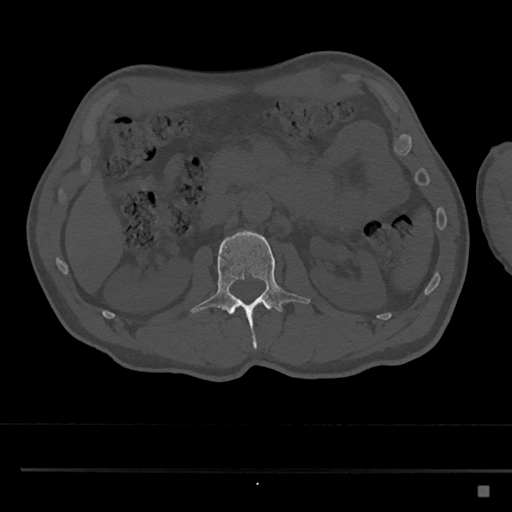
CT including the spine, one axial slice; slice 766 of 797 in the series (ordered by position); 120 kVp; bone window (W 1800 / L 400 HU); 0.5 mm slice thickness; 512 × 512 image matrix, field of view 391 × 391 mm. Patient: male, 59 years. Case-level facts recorded for this patient, not image findings: primary cancer: prostate.
Outlined on this slice (semi-automatic segmentation, software-assisted and operator-edited):
- L2 vertebra: box from (x=191, y=230) to (x=311, y=350) px